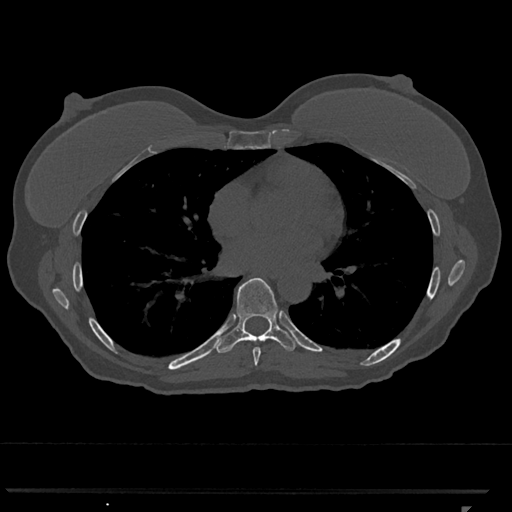
CT including the spine, one axial slice. Position 678 of 793 along the scan axis. Reconstruction kernel Br40s/3. 120 kVp. Bone window (W 1800 / L 400 HU). 0.5 mm slice thickness. 512 × 512 image matrix, field of view 380 × 380 mm. Female patient, age 62 years. Case-level facts recorded for this patient, not image findings: primary cancer: renal.
Annotated regions visible in this slice (semi-automatic segmentation, software-assisted and operator-edited):
- T7 vertebra: bounding box (x1, y1, x2, y2) in pixels: (253, 347, 261, 366)
- T8 vertebra: (215, 278, 297, 353)